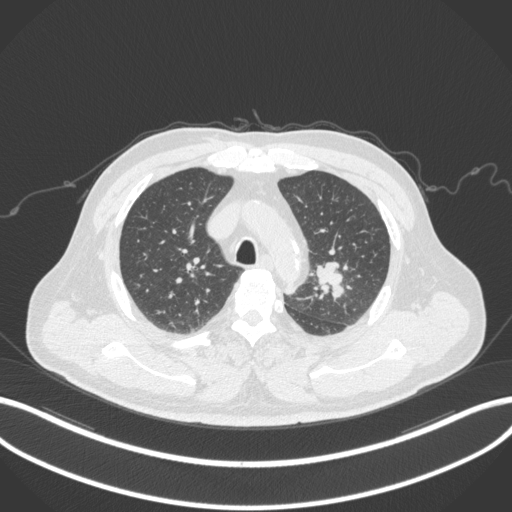
Chest CT, one axial slice. Slice 229 of 286 in the series (ordered by position). Lung window (W 1500 / L -600 HU). 512 × 512 image matrix. Patient: male, 67 years. Case-level facts recorded for this patient, not image findings: clinical TNM (as recorded): T2a N1 M0; histopathological grade: G3.
Annotated regions visible in this slice (bounding box drawn by a radiologist):
- lung tumour (recorded histology: adenocarcinoma): bounding box <311,256,348,304> (left, top, right, bottom; pixels)